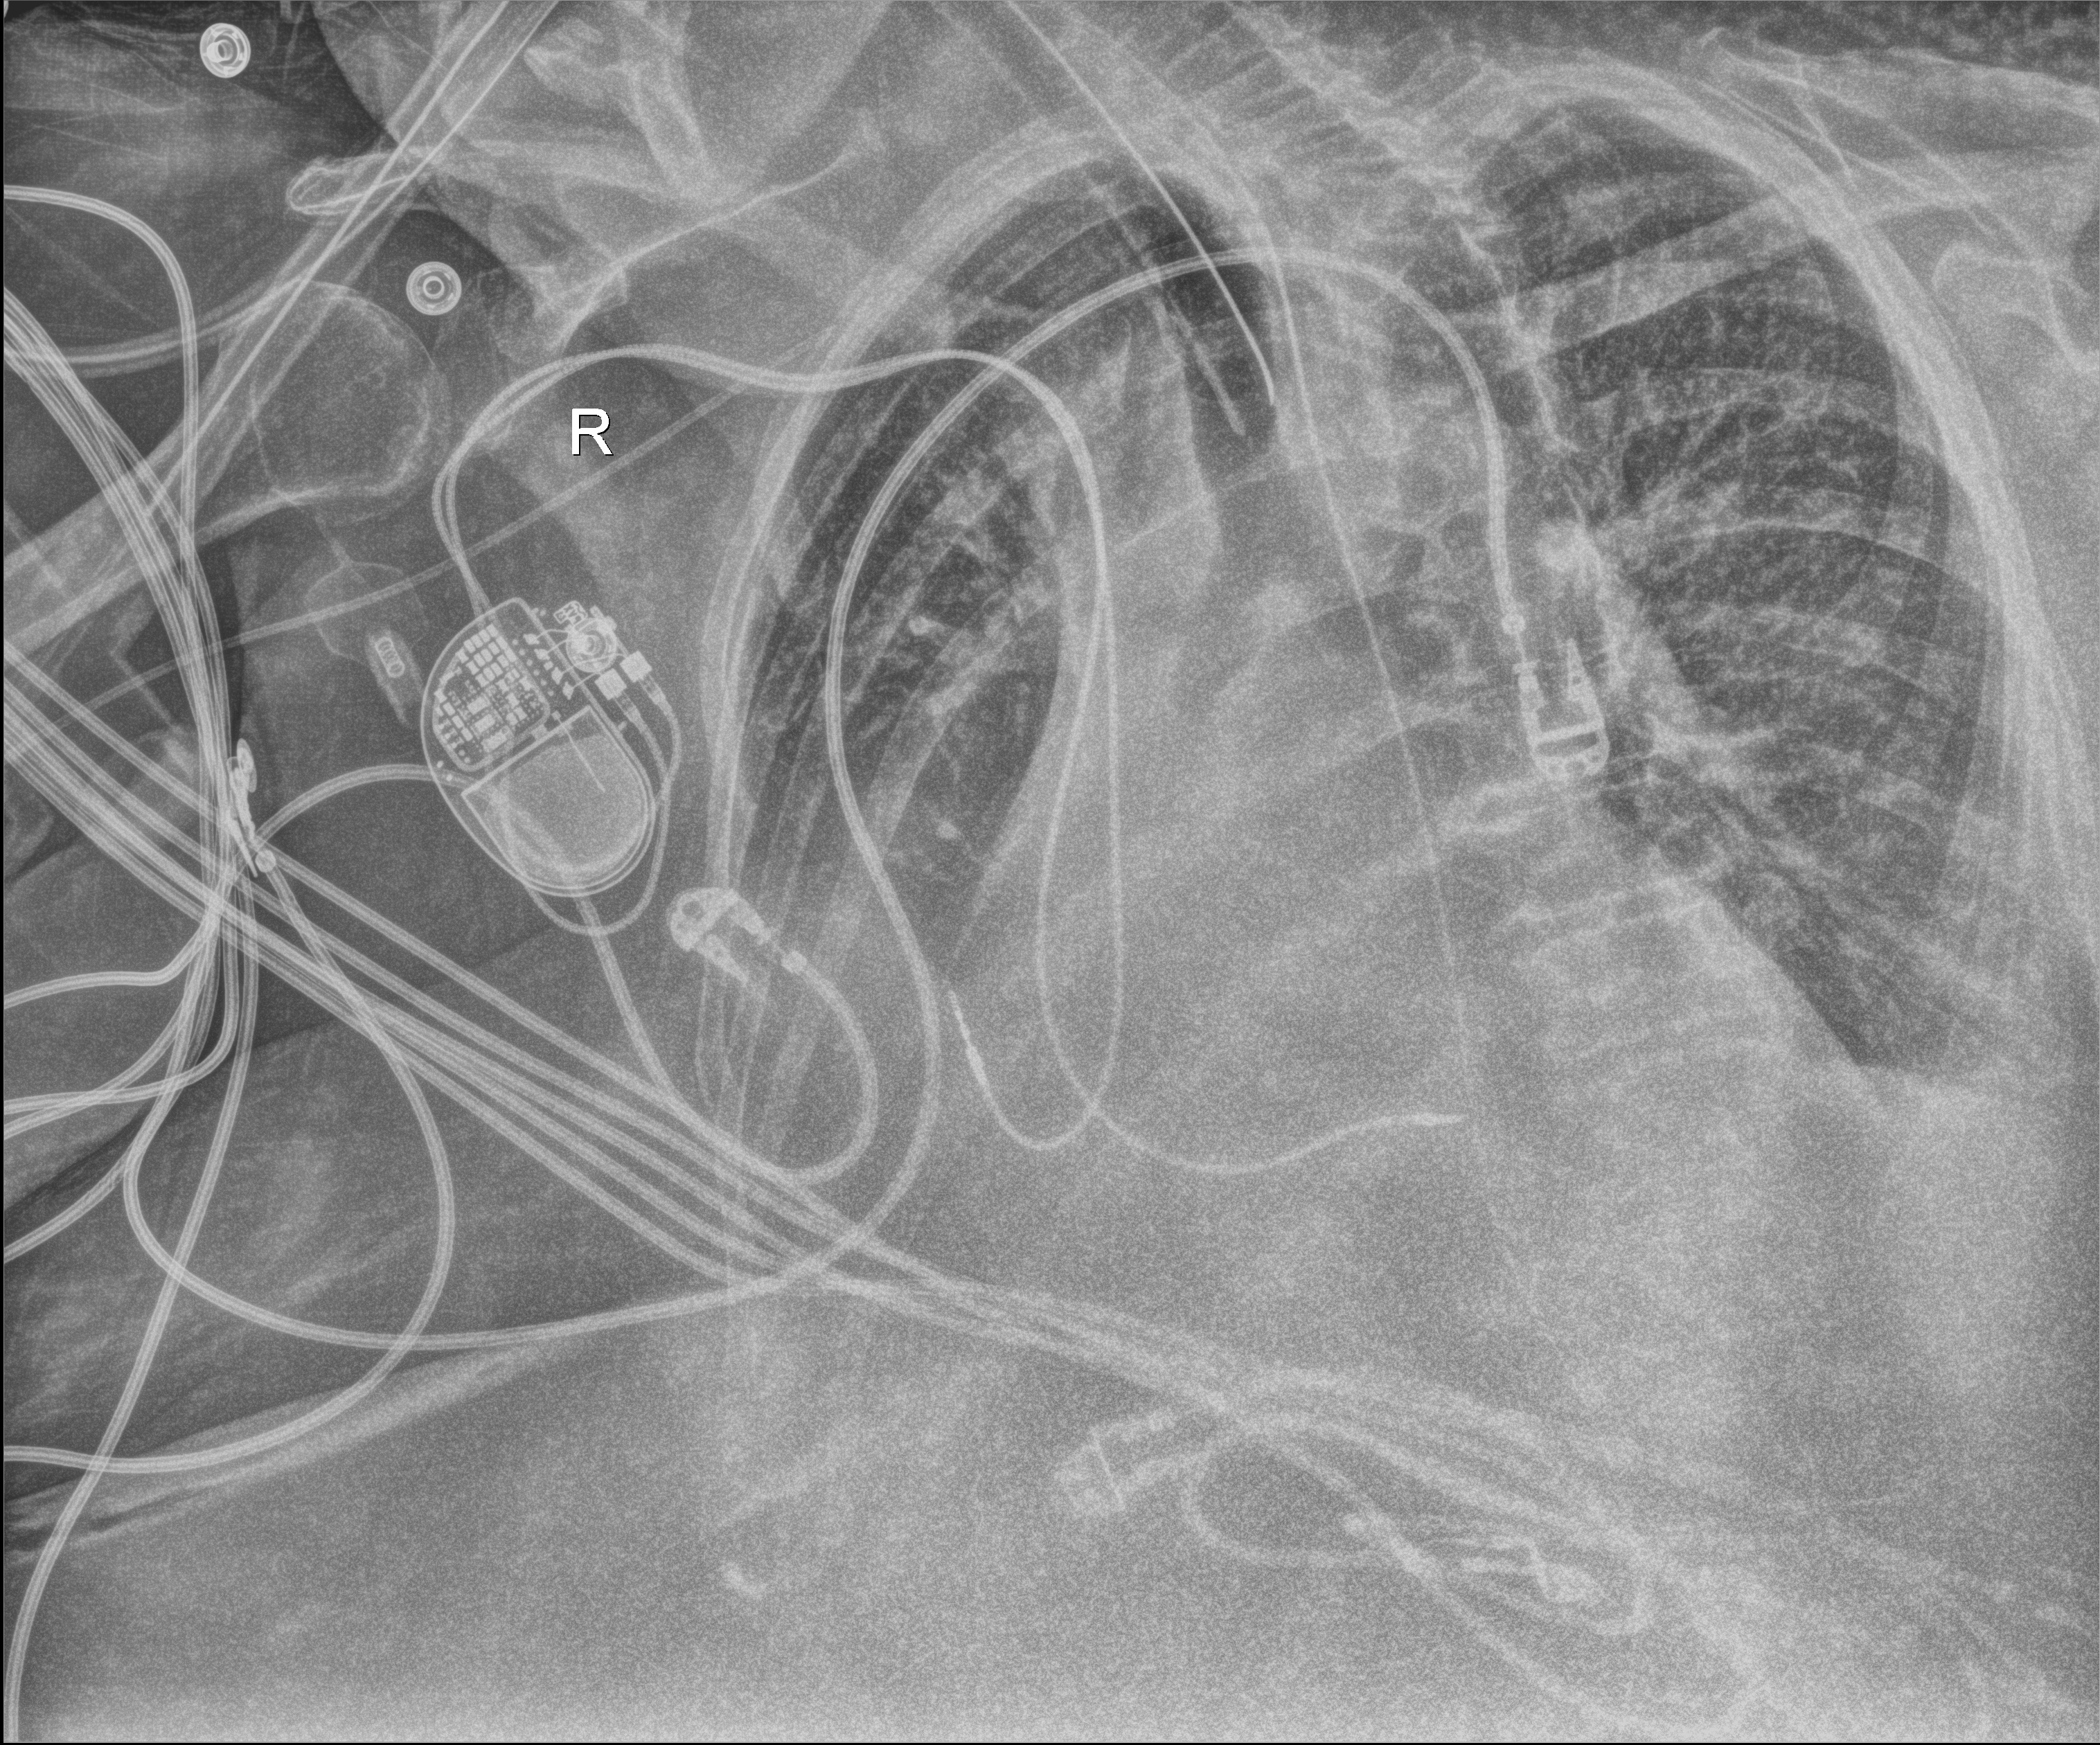
Portable chest radiograph, anteroposterior (AP) projection. Patient hospitalised with COVID-19; female, aged 75–90 years.
Admission-level facts for this patient (not findings on this image; timing relative to this image not recorded):
- length of hospital stay: 21 days